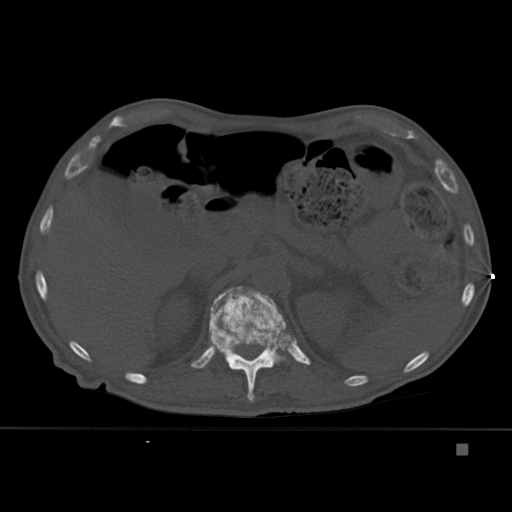
CT including the spine, one axial slice; slice 198 of 451 in the series (ordered by position); bone window (W 1800 / L 400 HU); 1.5 mm slice thickness; 512 × 512 image matrix. Male patient, age 75 years. Case-level facts recorded for this patient, not image findings: primary cancer: prostate.
Annotated regions visible in this slice (semi-automatic segmentation, software-assisted and operator-edited):
- T12 vertebra: bounding box <209,286,286,402> (left, top, right, bottom; pixels)